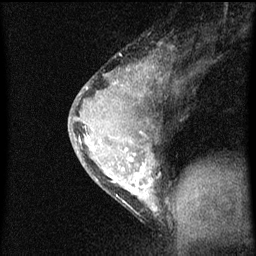
Breast MRI (dynamic contrast-enhanced), one sagittal slice; position 39 of 60 along the scan axis; dynamic contrast-enhanced series, image 2 of 3 at this slice position (ordered by acquisition); 1.5 T; TE 4.2 ms, TR 8 ms; 2 mm slice thickness; 256 × 256 image matrix, field of view 180 × 180 mm. Patient: female, 33 years.
Outlined on this slice (semi-automatic segmentation, software-assisted and operator-edited):
- analysis volume of interest (the breast-tissue region the enhancement analysis was run in; not a lesion): bounding box <69,56,172,215> (left, top, right, bottom; pixels)
- tumour enhancement mask (voxels above the 70 % enhancement threshold inside the analysis volume of interest): <80,66,158,211>